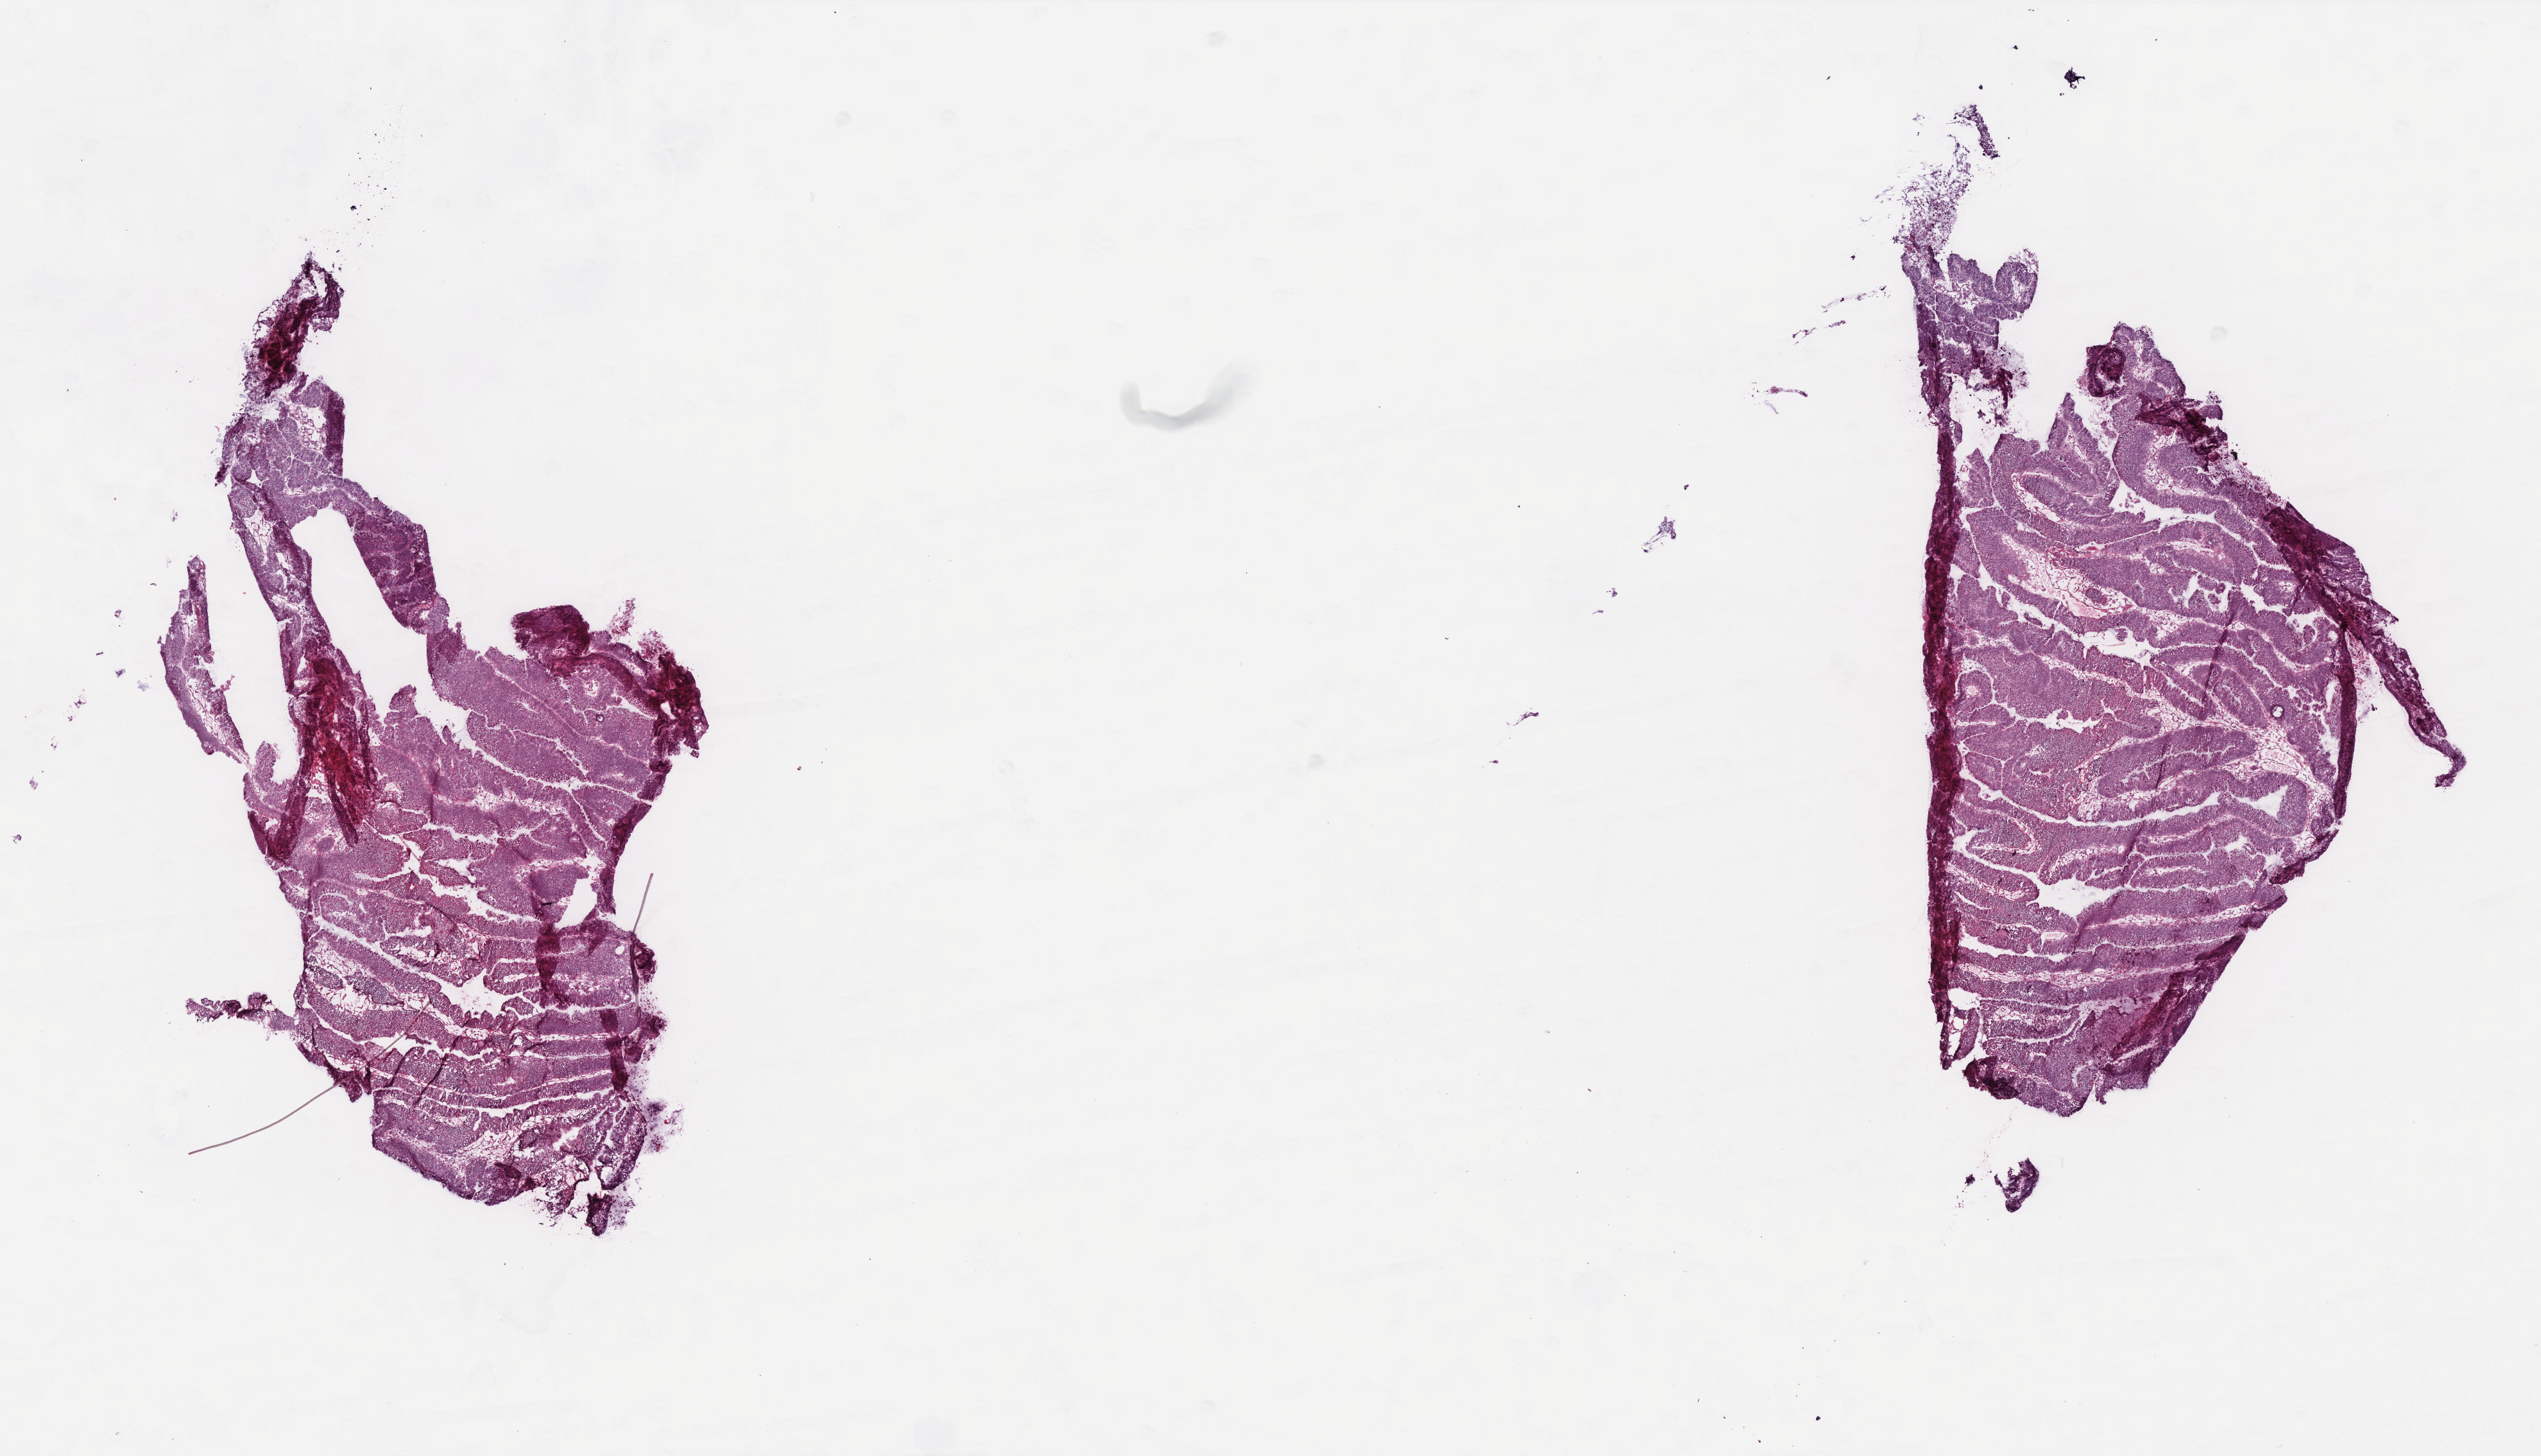
Digitized Hematoxylin and eosin (H&E) stained tissue section (whole slide) — a low-resolution overview of the entire scanned area, about 15.9 x 9.1 mm. Frozen section. Sample: primary tumour, rectum. Female, age 50 years at initial diagnosis. Slide review estimates, as recorded: tumour cells 95%, tumour nuclei 95%, normal cells 0%, stromal cells 4%, necrosis 1%. Infiltration values recorded for this section: lymphocyte infiltration 1%, monocyte infiltration 1%, neutrophil infiltration 1%.
* lymph nodes positive (case pathology): 0 of 28 examined
* AJCC pathologic stage: I (6th edition)
* histologic diagnosis: Mucinous adenocarcinoma
* TNM: T2 N0 M0